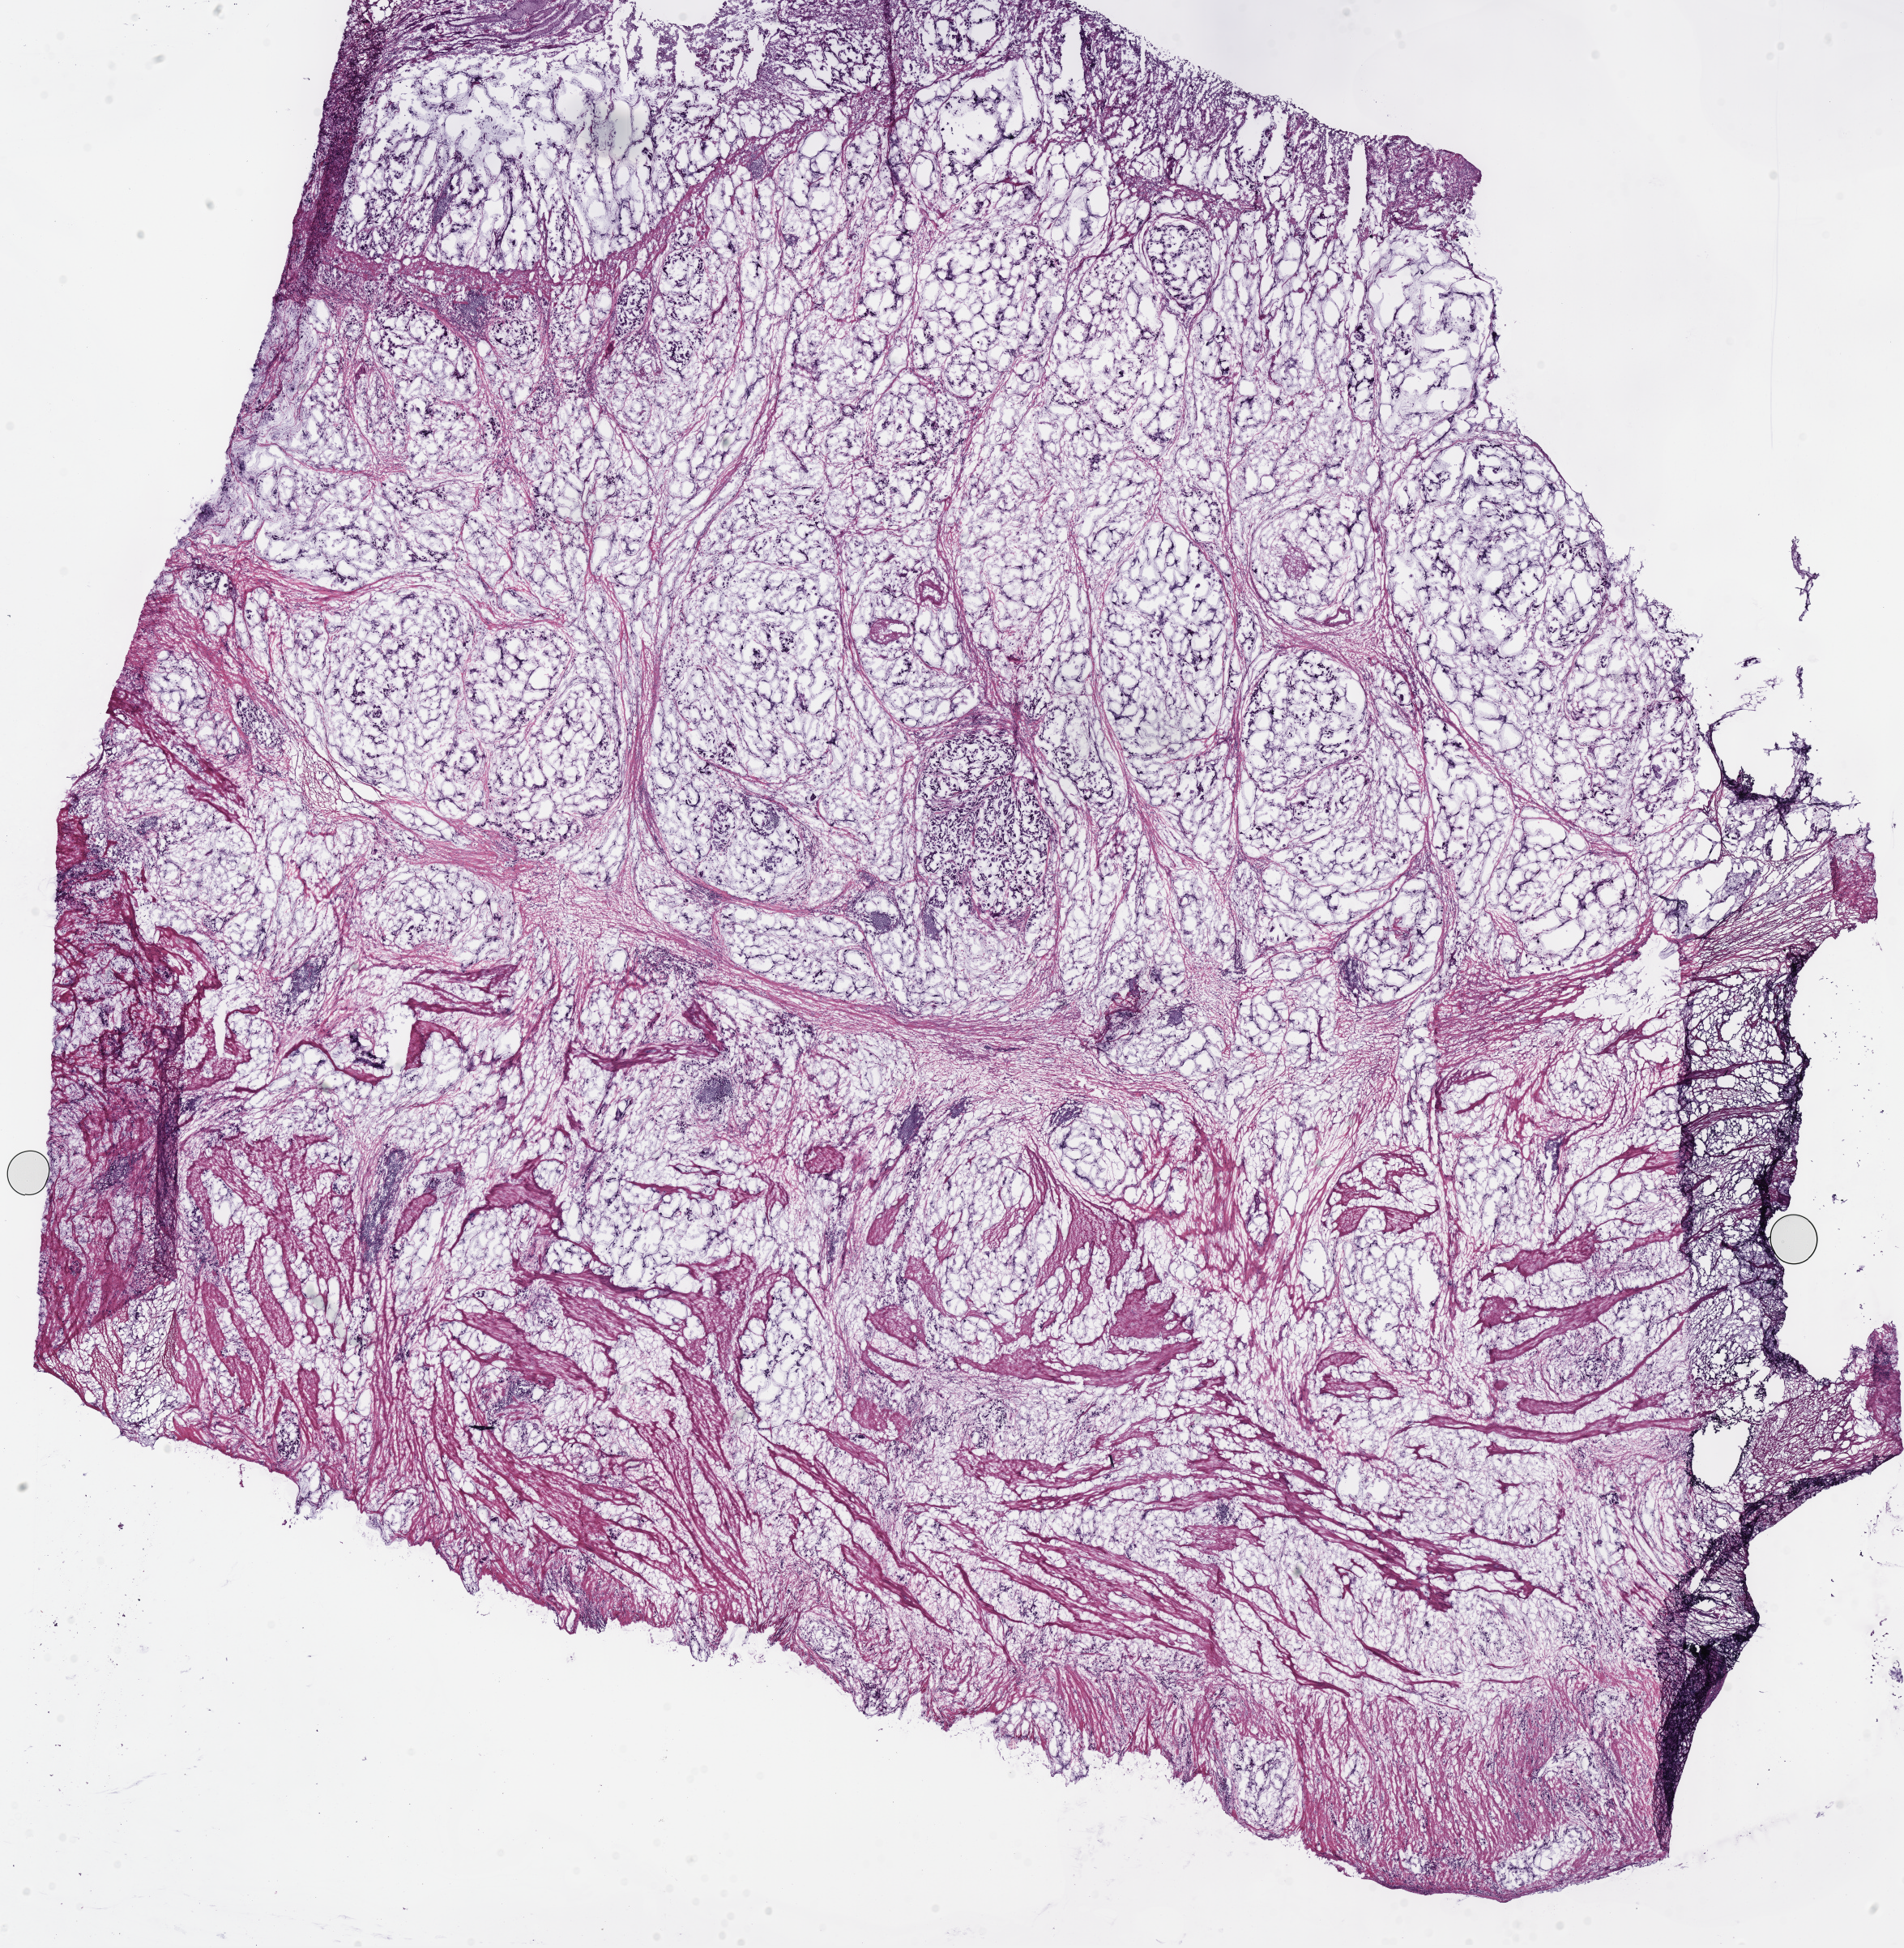
Hematoxylin and eosin (H&E) stained whole-slide image — shown as a low-resolution overview of the whole scanned area (about 18.5 x 18.9 mm, from a 40x scan). Frozen section. Sample: primary tumour, stomach. Female, age 72 years at initial diagnosis. Histologic grade: G3 (poorly differentiated). Slide review estimates, as recorded: tumour cells 98%, tumour nuclei 61%, normal cells 2%, stromal cells 0%, necrosis 0%. Infiltration values recorded for this section: lymphocyte infiltration 15%, monocyte infiltration 5%, neutrophil infiltration 5%.
- TNM: T4 N3a M0
- AJCC pathologic stage: IIIC (7th edition)
- lymph nodes positive (case pathology): 10 of 12 examined
- diagnosis: Mucinous adenocarcinoma (body of stomach)